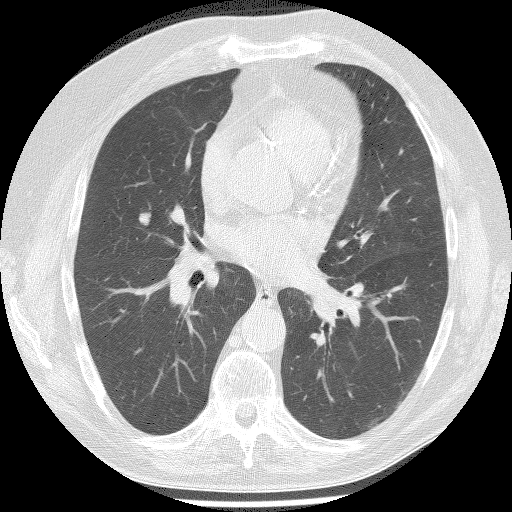
Axial slice from a low-dose chest CT screening exam, second screening round (one year after baseline), lung window (W 1500 / L -600 HU), lung (sharp) reconstruction kernel (BONE), 120 kVp, 512 × 512 image matrix. Male participant, aged 61 years at enrolment.
Expert reader's lesion annotation, bounding box (x1, y1, x2, y2) in pixels: (123, 200, 158, 237). The screening reader recorded 2 non-calcified nodules or masses ≥4 mm on this exam (right upper lobe, right lower lobe); which of them this box marks is not recorded. Official screen result: positive, other. Lung cancer was diagnosed 147 days after this screen: bronchiolo-alveolar adenocarcinoma, NOS, right middle lobe, well differentiated (G1), stage IA (AJCC 6th edition), 15 mm at pathology.